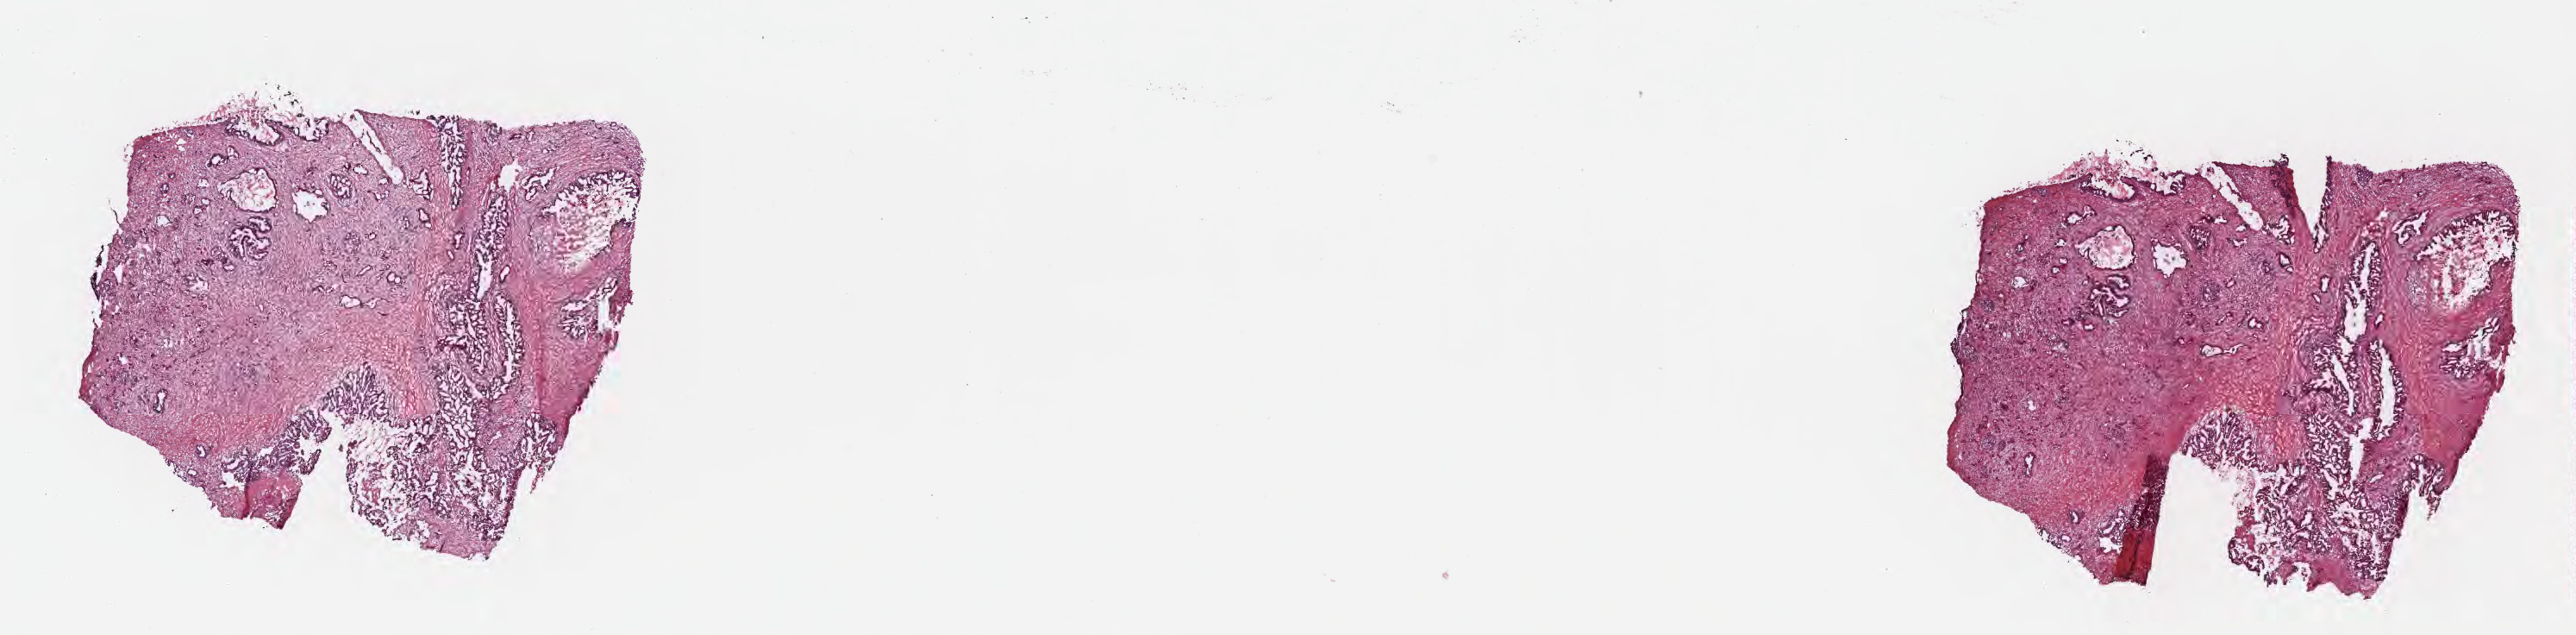
Whole-slide image, hematoxylin and eosin (H&E) stain — shown as a low-resolution overview of the whole scanned area (about 24.1 x 5.9 mm). Cryosection. Primary tumor. Site: body of pancreas. Patient: male, age at initial diagnosis 66 years. Tumor grade: G2 (moderately differentiated). Composition of this section per pathologist review: tumor cells 60%, tumor nuclei 60%, stromal cells 17%, necrosis 3%, normal cells 20%. Inflammatory infiltration, as recorded: lymphocyte infiltration 7%, monocyte infiltration 1%, neutrophil infiltration 4%.
AJCC pathologic stage: Stage III. Section: bottom of the tissue portion. Histologic diagnosis: Infiltrating duct carcinoma, NOS.